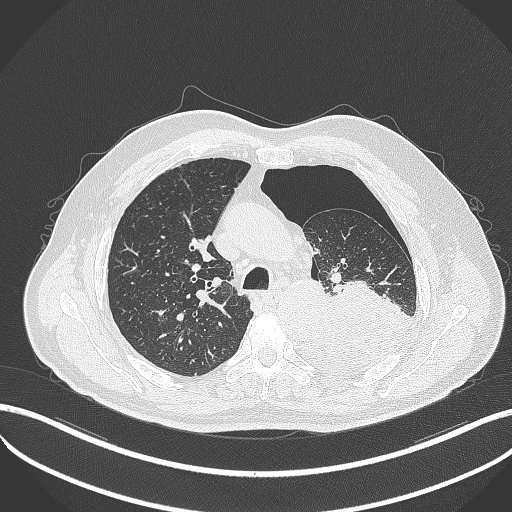
Chest CT, one axial slice; position 359 of 464 along the scan axis; 120 kVp; lung window (W 1500 / L -600 HU); 1 mm slice thickness; 512 × 512 image matrix, field of view 400 × 400 mm. Male patient, age 76 years. From the clinical record (not read from this slice): clinical TNM (as recorded): T3 N0 M1b.
Outlined on this slice (rectangle marked by the reading radiologist):
- lung tumour (recorded histology: adenocarcinoma): bounding box (x1, y1, x2, y2) in pixels: (302, 276, 415, 373)